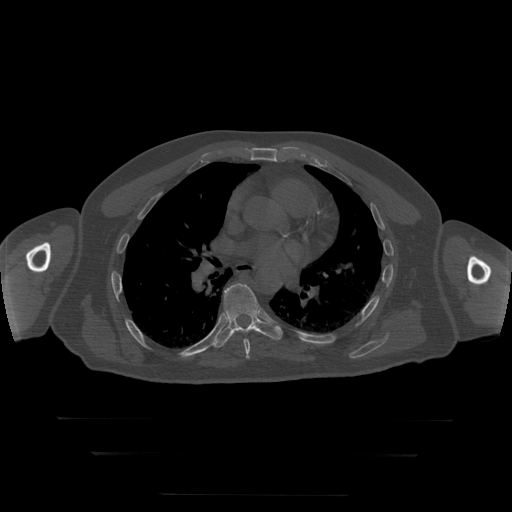
CT including the spine, one axial slice; position 173 of 397 along the scan axis; 120 kVp; bone window (W 1800 / L 400 HU); 512 × 512 image matrix, field of view 510 × 510 mm. Patient age 73 years. Case-level facts recorded for this patient, not image findings: primary cancer: prostate.
Outlined on this slice (semi-automatically segmented with operator editing):
- T7 vertebra: bounding box [x1, y1, x2, y2] px = [244, 339, 250, 359]
- T8 vertebra: [211, 284, 283, 348]